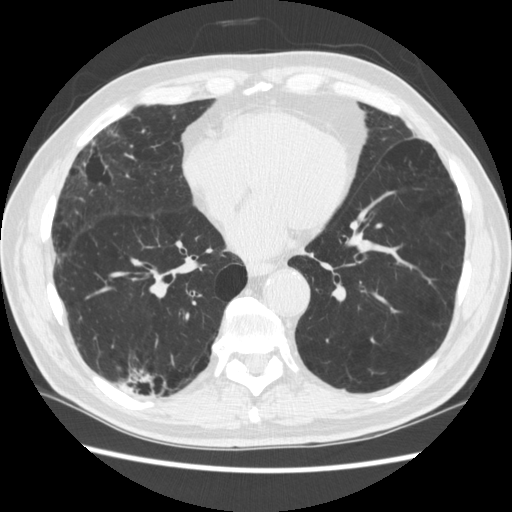
Axial slice from a low-dose chest CT screening exam. Third screening round (two years after baseline). Lung window (W 1500 / L -600 HU). 1.25 mm slice thickness. 120 kVp. Slice 159 of 266 in the series. Male, age 70 years at enrolment. Former smoker at enrolment.
Expert-annotated lung lesion, bounding box (x1, y1, x2, y2) in pixels: (128, 359, 178, 414). The screening reader recorded 4 non-calcified nodules or masses ≥4 mm on this exam (right lower lobe, right lower lobe, left lower lobe, left lower lobe); which of them this box marks is not recorded. Official screen result: positive, other. Lung cancer was diagnosed 253 days after this screen: squamous cell carcinoma, NOS, right upper lobe, poorly differentiated (G3), stage IV (AJCC 6th edition).